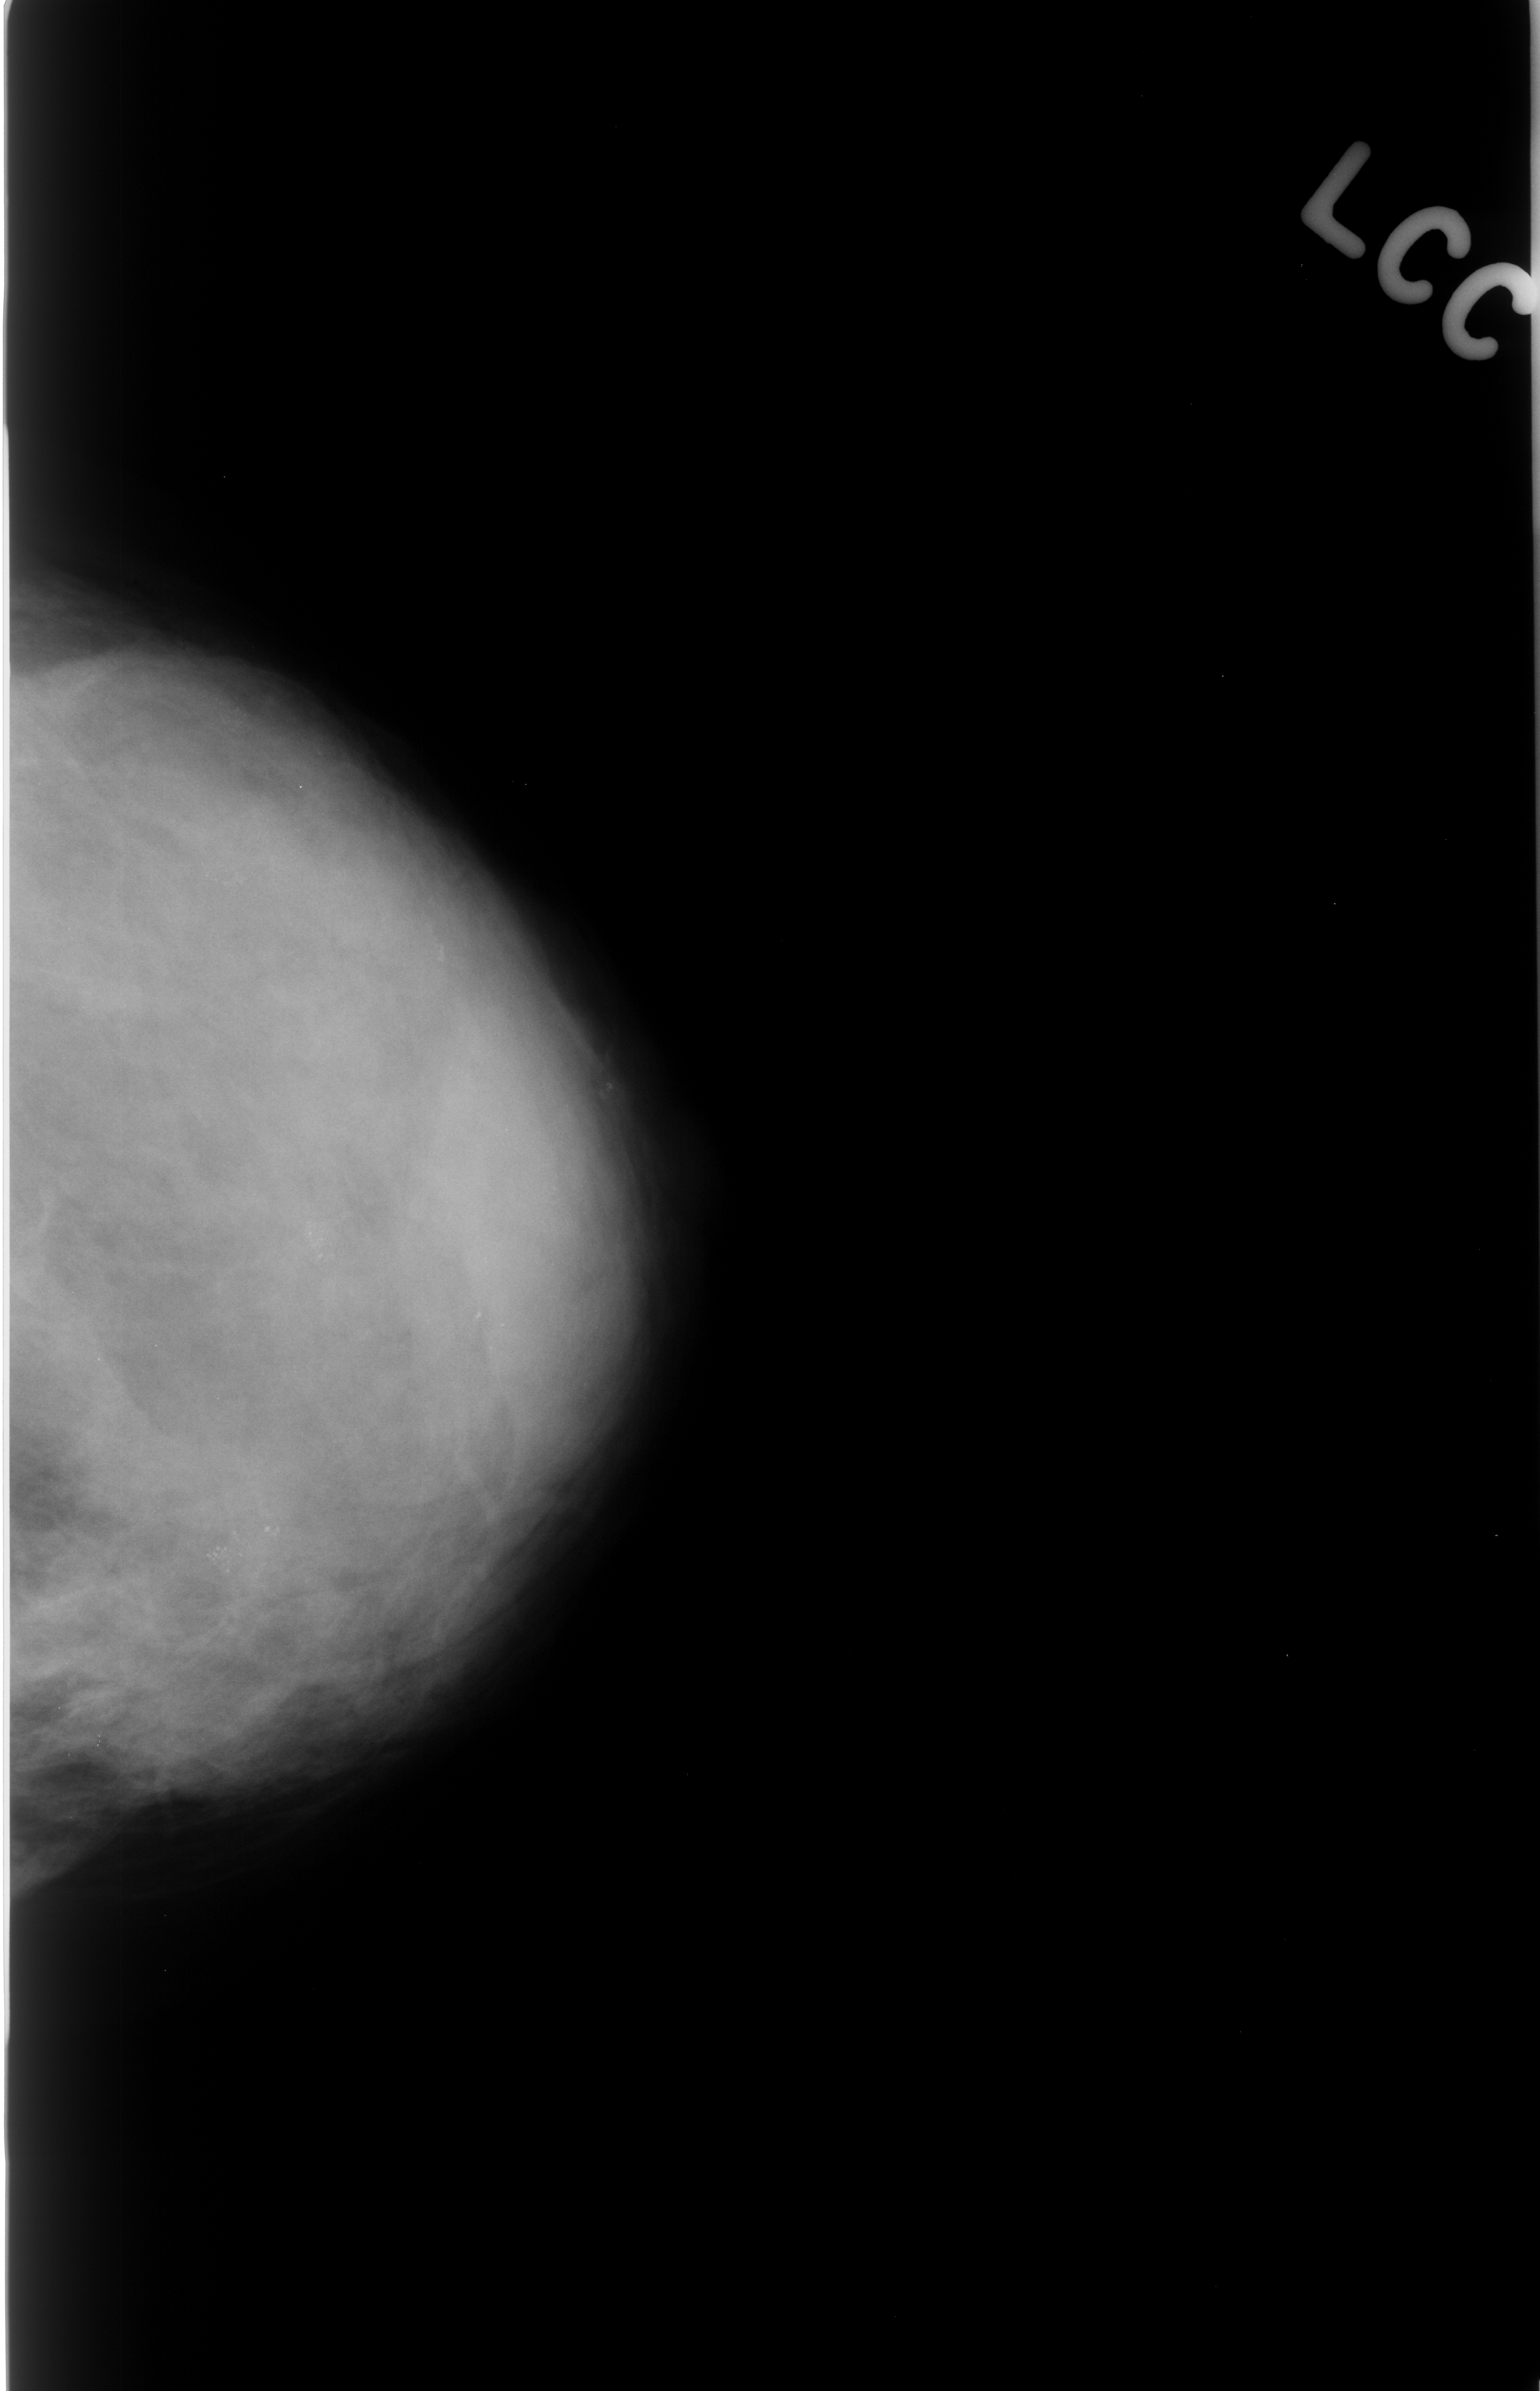
Mammogram (digitized film), left breast, CC view, BI-RADS breast density category 4 (scale 1–4).
Marked findings (only marked abnormalities are described; nothing is implied about the rest of the image): Finding 1 of 2: calcifications, morphology pleomorphic, distribution clustered; BI-RADS assessment category 4; subtlety rating 4 on a 1 (subtle) to 5 (obvious) scale; pathology result (as recorded, not read from the image): benign. Finding 2 of 2: calcifications, morphology pleomorphic, distribution clustered; BI-RADS assessment category 4; pathology (as recorded): benign.